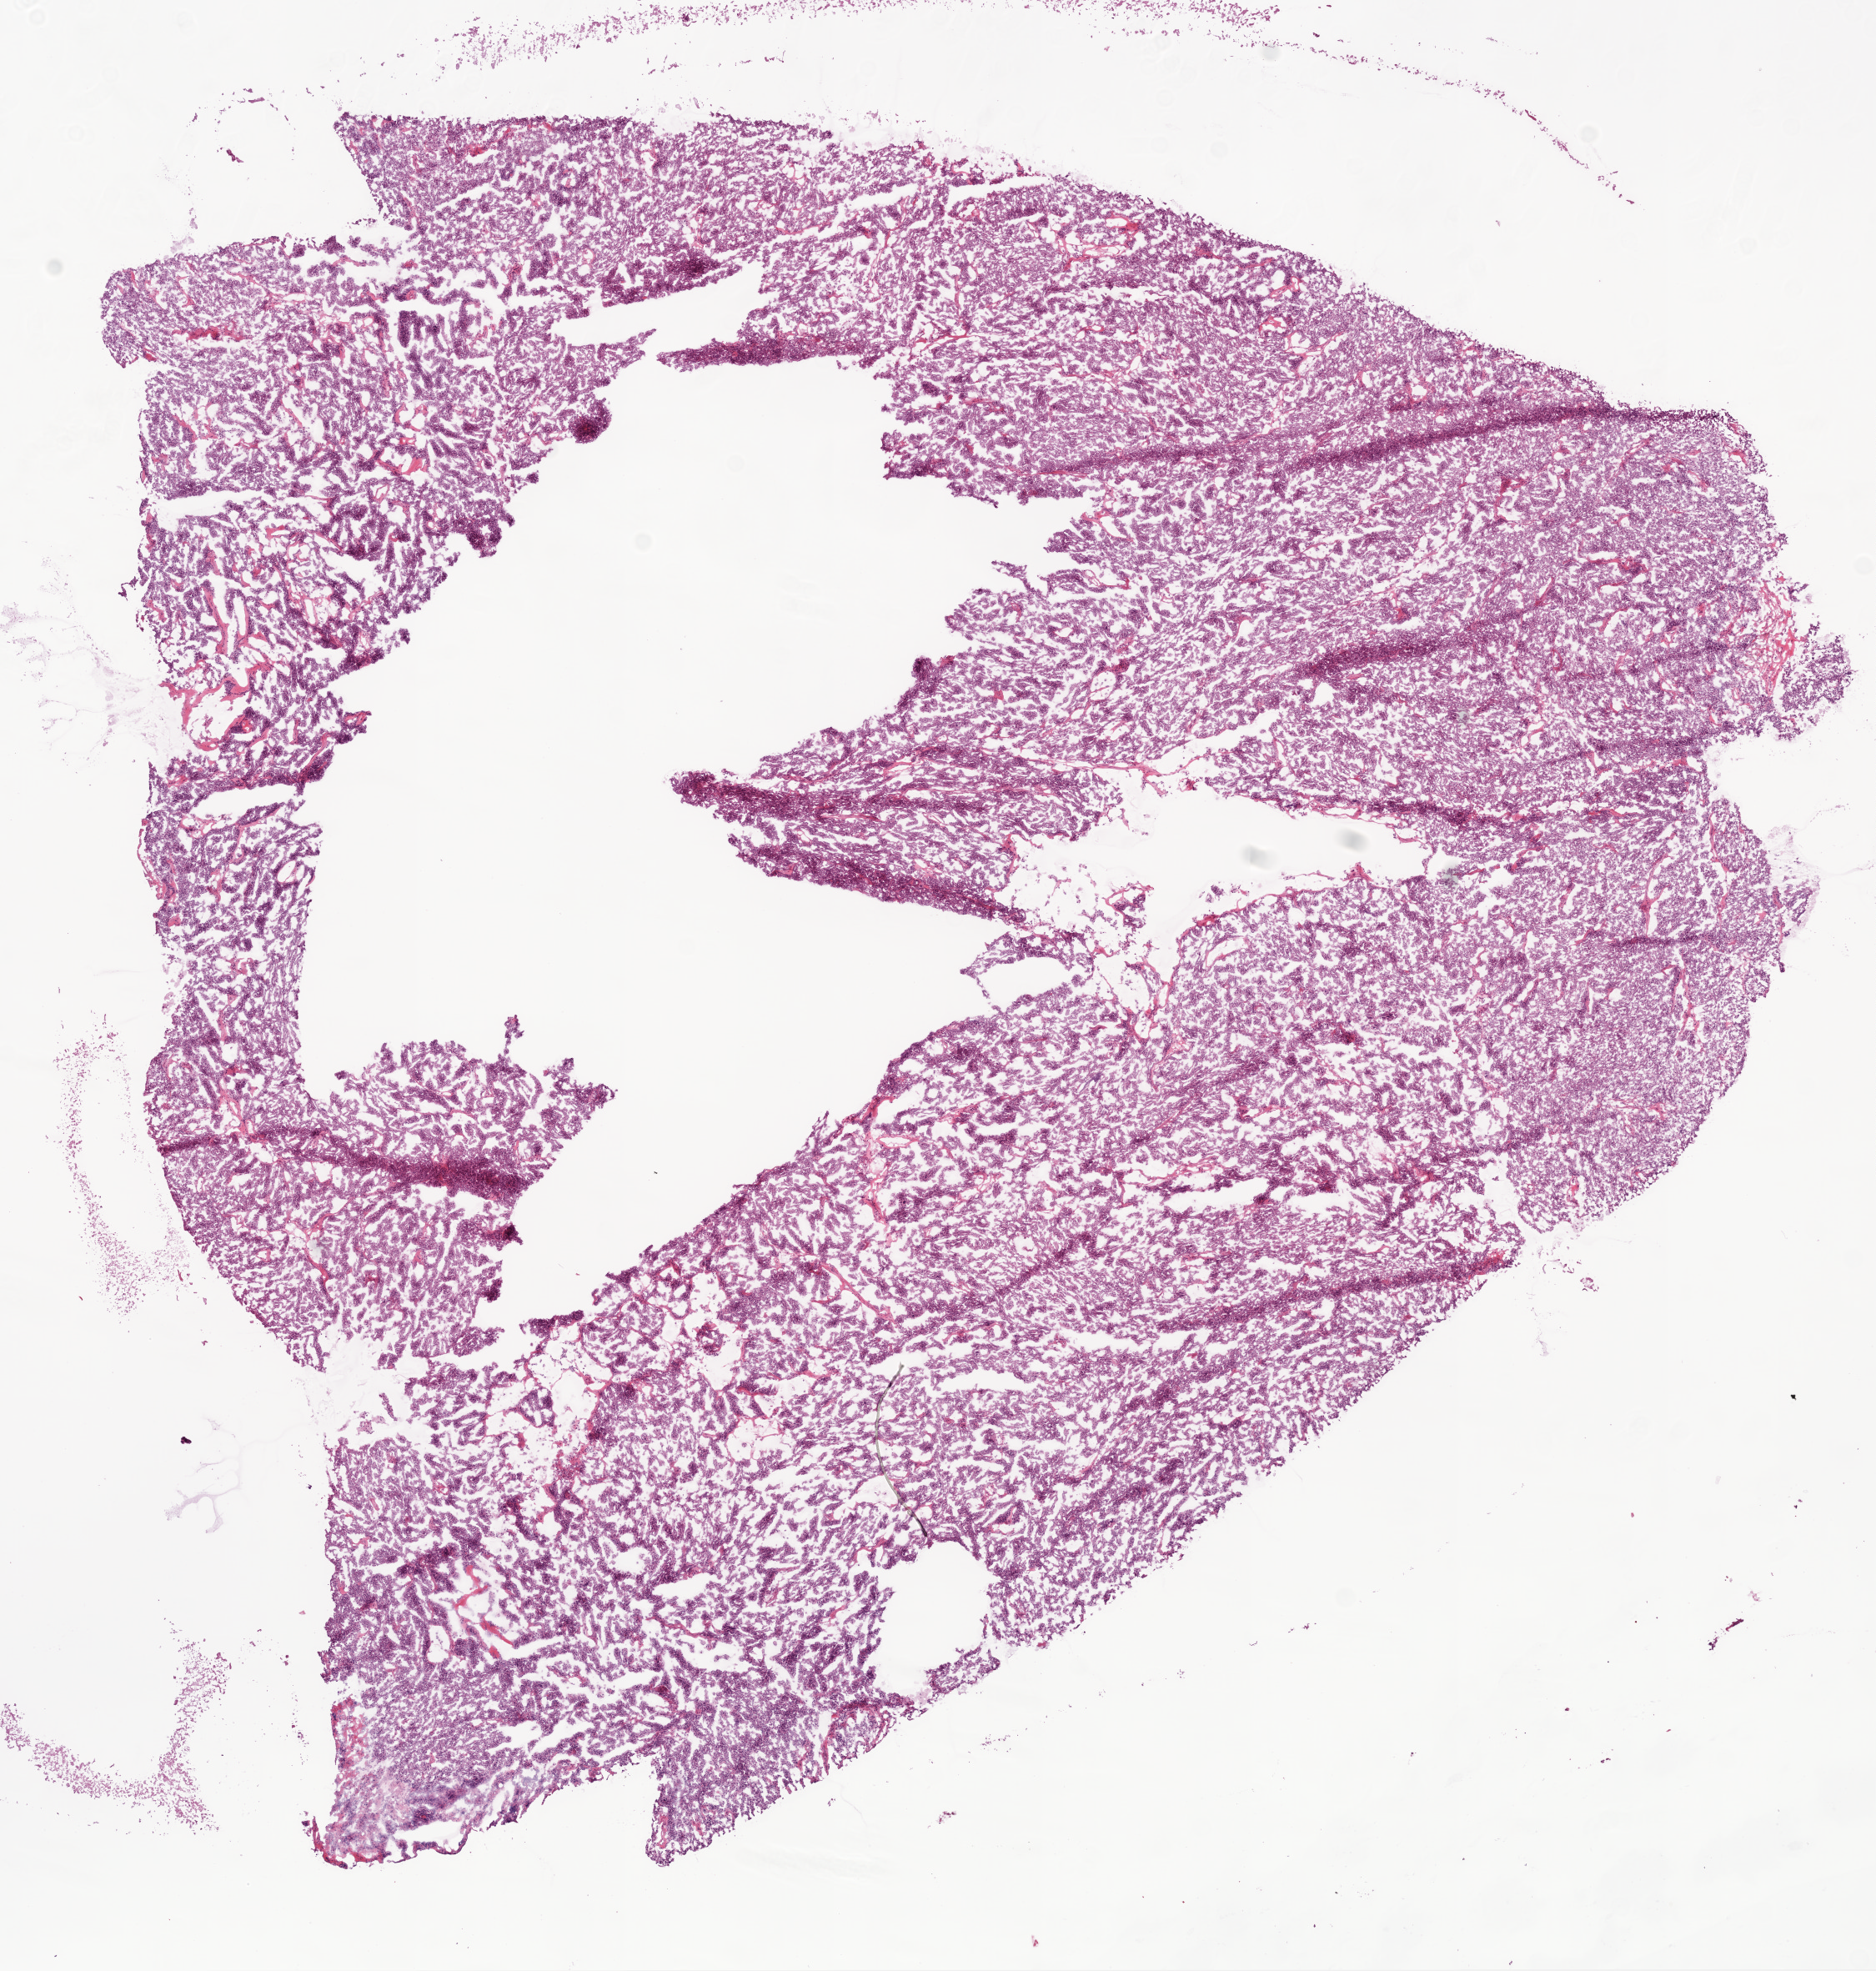
Whole-slide histology image, H&E-stained, a low-resolution overview of the entire scanned area, about 9.0 x 9.5 mm (acquisition: 20x scan), frozen section from the bottom of the tissue portion, ovary, recurrent tumour sample. Female patient; age at initial diagnosis 61 years. Pathologist review of this section (percent, as recorded): tumour cells 90%, tumour nuclei 90%, normal cells 0%, stromal cells 5%, necrosis 5%.
- this section: recurrent tumour
- patient diagnosis: Serous cystadenocarcinoma, NOS